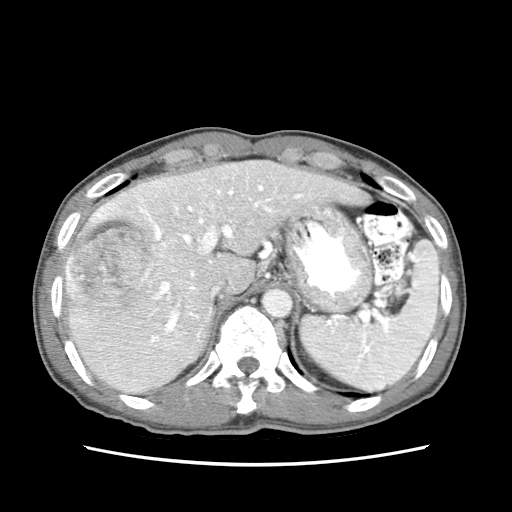
Contrast-enhanced abdominal CT (liver protocol), one axial slice. Position 51 of 79 along the scan axis. Reconstruction kernel STANDARD. Soft-tissue window (W 400 / L 40 HU). 512 × 512 image matrix, field of view 320 × 320 mm. From the clinical record (not read from this slice): diagnosis: hepatocellular carcinoma (patient treated with transarterial chemoembolisation; whether this scan precedes or follows treatment is not stated here); TNM stage (as recorded): Stage-IIIB; Child-Pugh class: A; tumour differentiation: moderately differentiated; tumour nodularity: multinodular.
Annotated regions visible in this slice (semi-automatically segmented with operator editing):
- liver parenchyma outside the tumour (the mass and vessels are separate outlines, so this box may not span the whole liver): bounding box (x1, y1, x2, y2) in pixels: (62, 158, 370, 392)
- mass: (62, 190, 169, 334)
- liver vessels: (103, 171, 306, 364)